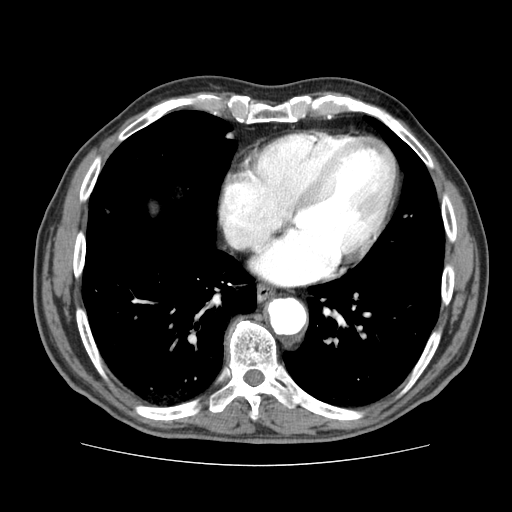
Contrast-enhanced abdominal CT (liver protocol), one axial slice. Position 77 of 79 along the scan axis. 120 kVp. Soft-tissue window (W 400 / L 40 HU). 2.5 mm slice thickness. 512 × 512 image matrix, field of view 360 × 360 mm. Case-level facts recorded for this patient, not image findings: diagnosis: hepatocellular carcinoma (patient treated with transarterial chemoembolisation; whether this scan precedes or follows treatment is not stated here); TNM stage (as recorded): Stage-I; Child-Pugh class: A; tumour nodularity: uninodular.
Annotated regions visible in this slice (semi-automatic segmentation, software-assisted and operator-edited):
- abdominal aorta: bounding box (x1, y1, x2, y2) in pixels: (269, 298, 305, 333)